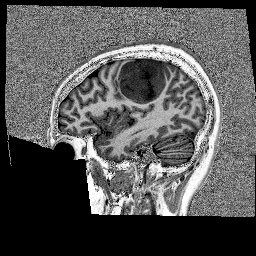
Brain MRI from a brain-tumour surgery series, one sagittal slice. Position 50 of 176 along the scan axis. 1 mm slice thickness. 256 × 256 image matrix, field of view 256 × 256 mm. Case-level facts recorded for this patient, not image findings: histopathology: Glioblastoma; WHO grade: 4.
Annotated regions visible in this slice (expert manual segmentation):
- tumour: bounding box [x1, y1, x2, y2] px = [118, 58, 175, 105]